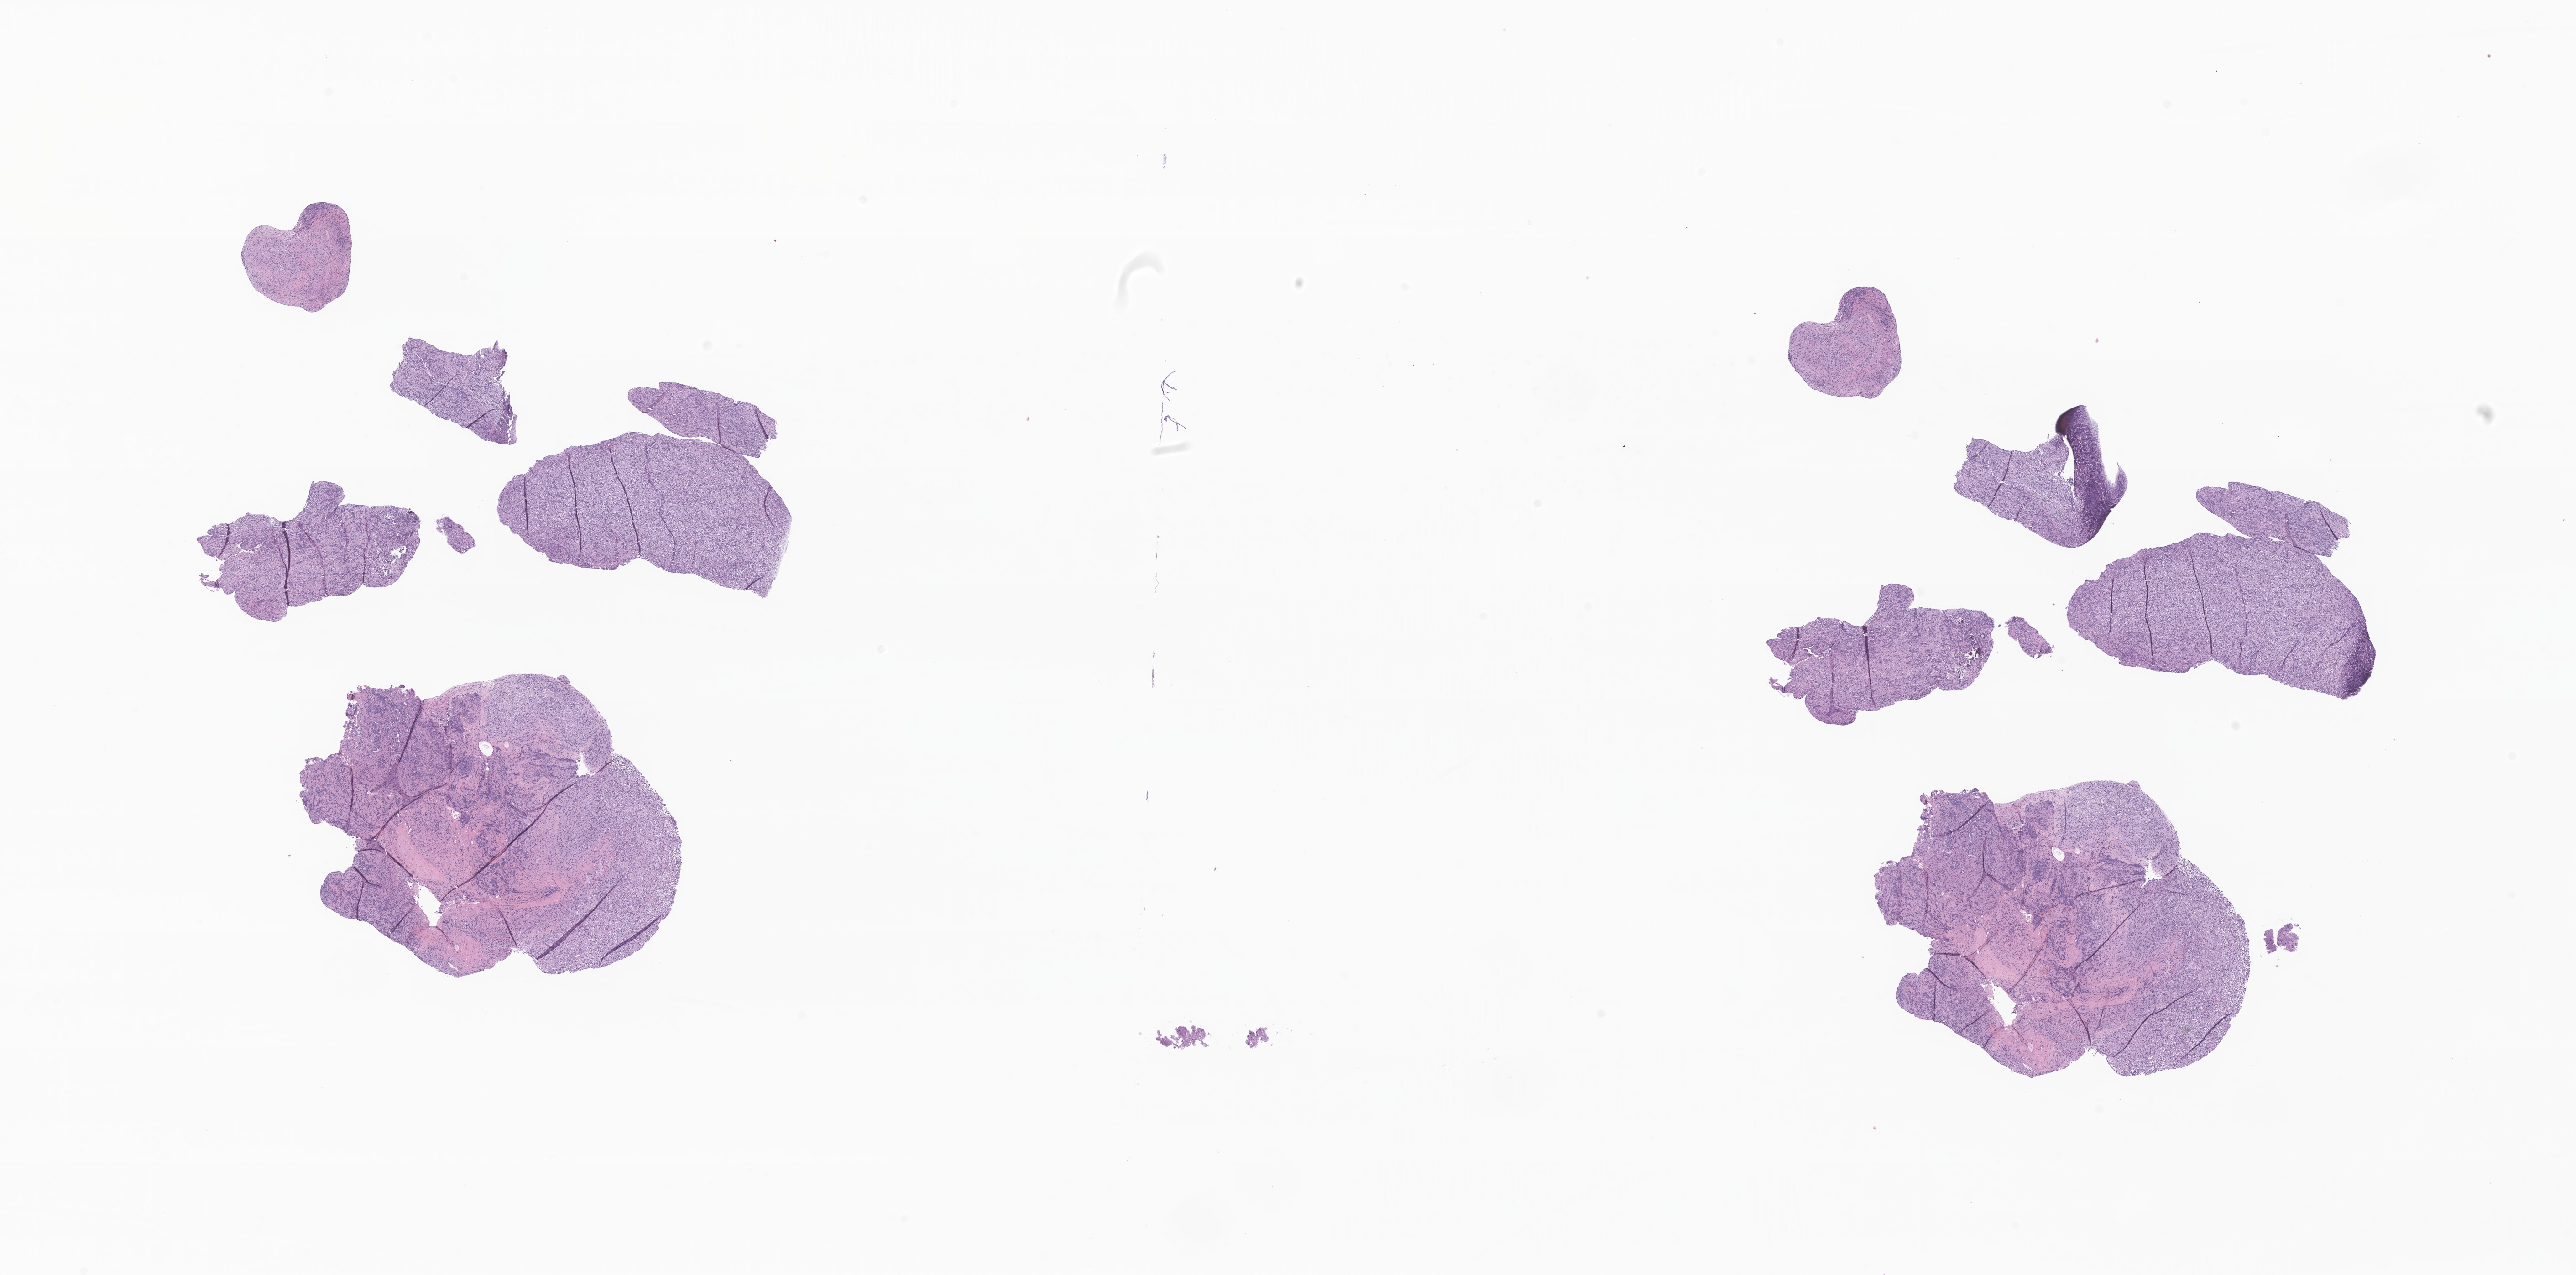
Hematoxylin and eosin (H&E) whole-slide image of tumor tissue from the pituitary gland, whole scanned area (about 23.8 x 11.8 mm) shown as a low-resolution overview, formalin-fixed, paraffin-embedded (FFPE) tissue. Male patient, age 197 months.
Recorded diagnosis: Pituitary adenoma, NOS.